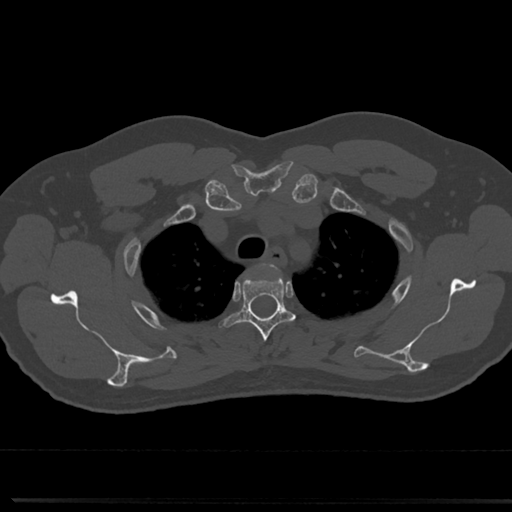
CT including the spine, one axial slice. 120 kVp. Bone window (W 1800 / L 400 HU). 0.5 mm slice thickness. 512 × 512 image matrix, field of view 355 × 355 mm. Male patient, age 61 years. From the clinical record (not read from this slice): primary cancer: prostate.
Outlined on this slice (semi-automatically segmented with operator editing):
- T3 vertebra: bounding box <232,266,293,348> (left, top, right, bottom; pixels)